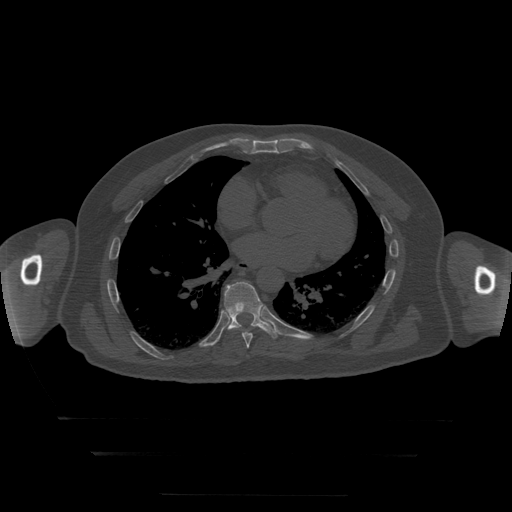
CT including the spine, one axial slice. Slice 154 of 397 in the series (ordered by position). Reconstruction kernel STANDARD. 120 kVp. Bone window (W 1800 / L 400 HU). 1.25 mm slice thickness. 512 × 512 image matrix, field of view 510 × 510 mm. Patient age 73 years. From the clinical record (not read from this slice): primary cancer: prostate.
Annotated regions visible in this slice (semi-automatic segmentation, software-assisted and operator-edited):
- T8 vertebra: box from (x=225, y=310) to (x=254, y=349) px
- T9 vertebra: (x=224, y=282)–(x=278, y=339)